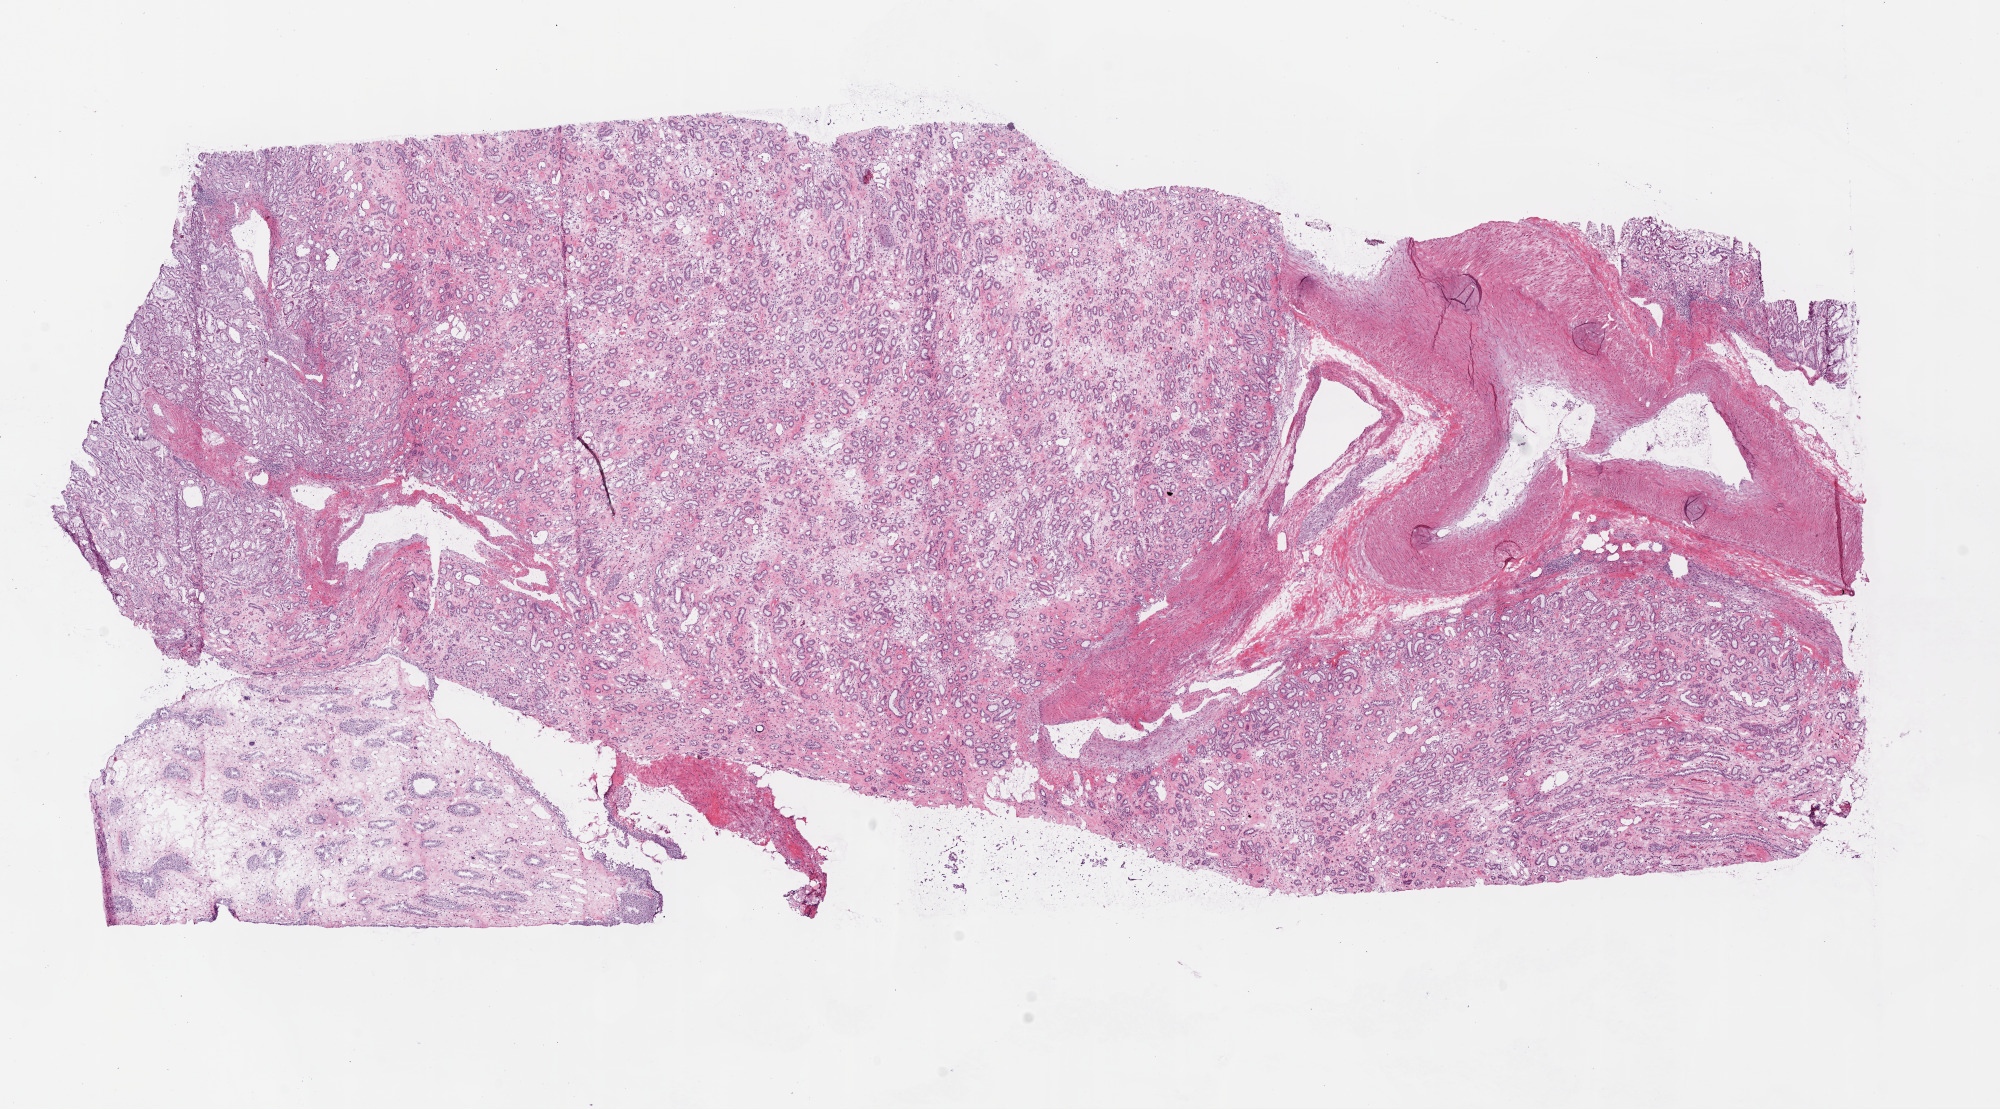
H&E whole-slide image, a low-resolution overview of the entire scanned area, about 16.0 x 8.9 mm (from a 20x scan). Frozen section. Kidney, solid tissue normal (non-tumour tissue) sample. Female, age 72 years at initial diagnosis.
This section: solid tissue normal sample (biorepository sample class). Patient diagnosis: Clear cell adenocarcinoma, NOS.